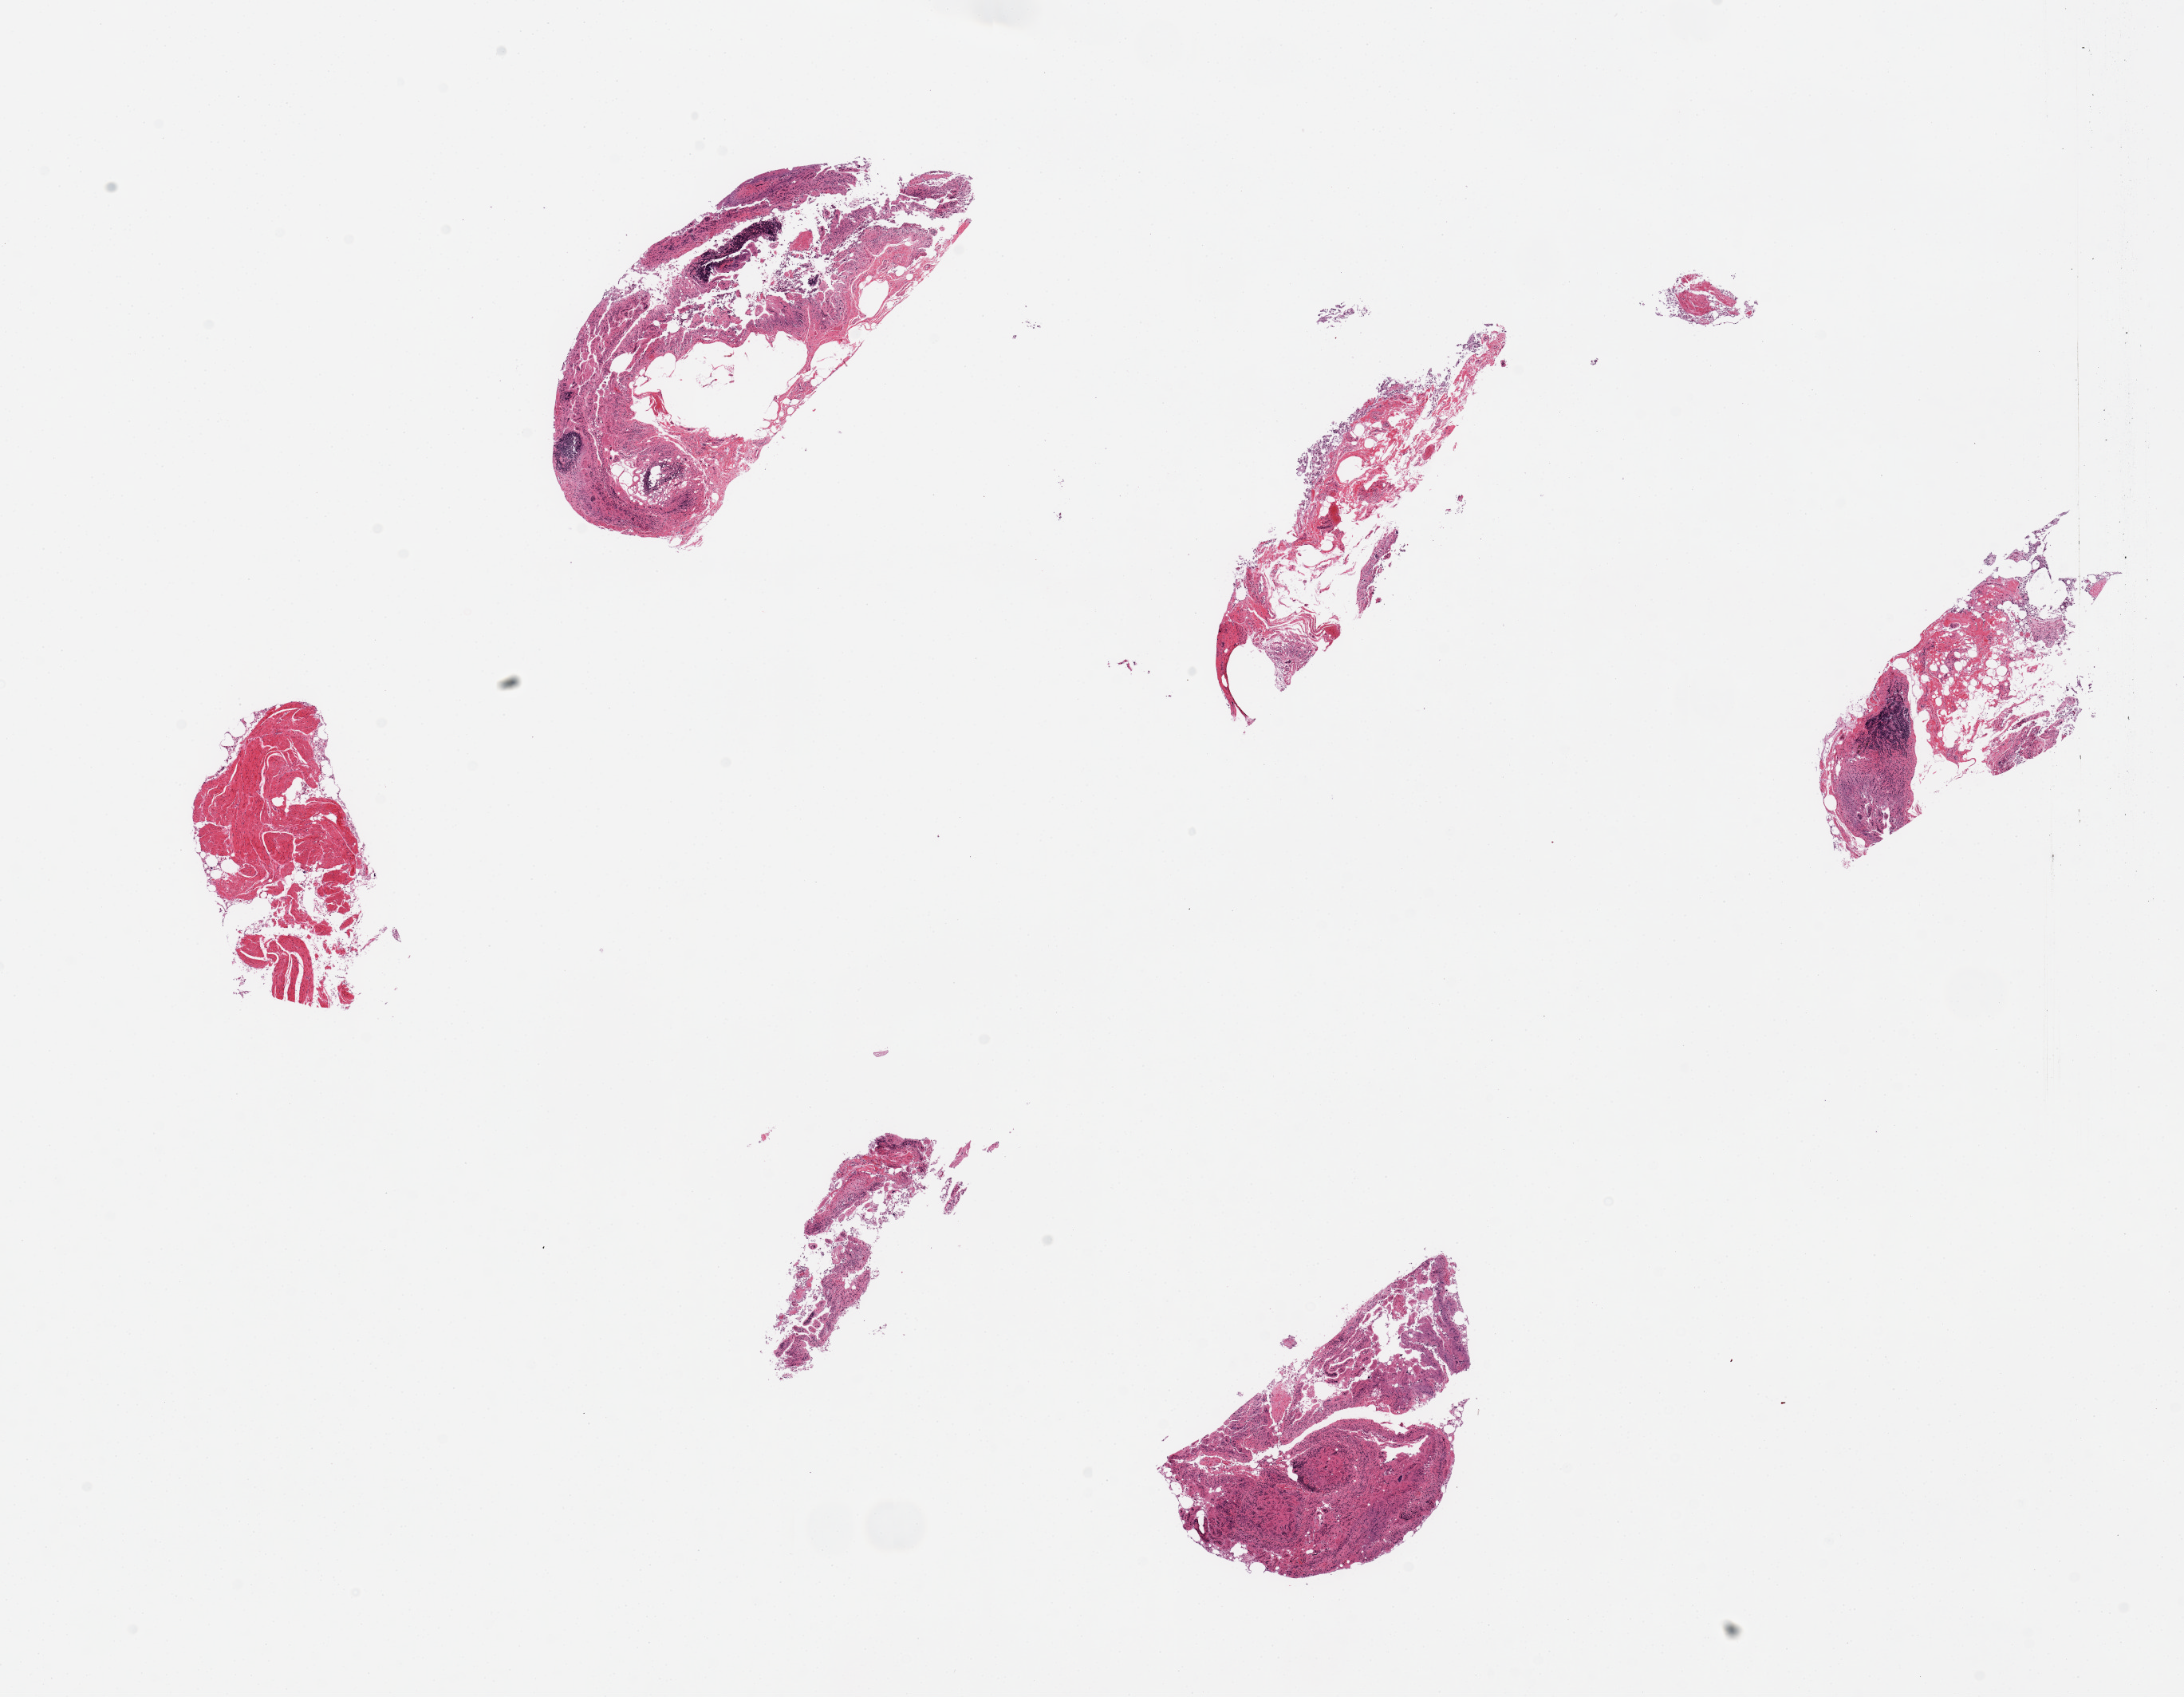
Whole-slide image, haematoxylin and eosin stain, brightfield, a low-resolution overview of the entire scanned area, about 21.7 x 16.8 mm (acquisition: 20x scan), PAXgene-fixed paraffin-embedded (PFPE) section, section of ileum (target tissue), tissue donor sample. Male donor.
Review note (as recorded): 6 pieces; insufficient lymphoid tissue.